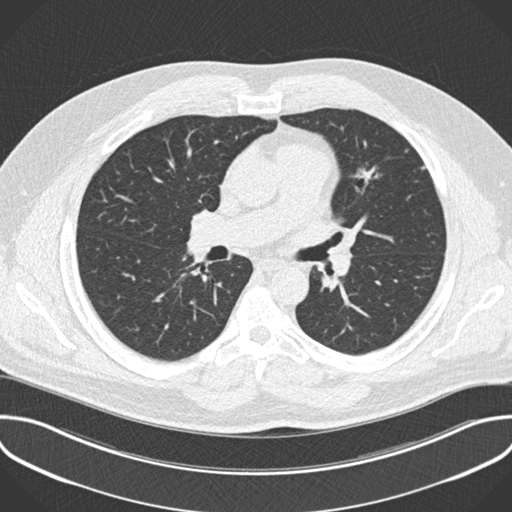
Low-dose screening chest CT, one axial slice; slice 124 of 201 in the series (ordered by position); reconstruction kernel B30f; 120 kVp; lung window (W 1500 / L -600 HU); 2 mm slice thickness; 512 × 512 image matrix, field of view 386 × 386 mm.
Structures marked on this image (expert manual segmentation):
- lesion 1 (tumor, upper lobe of left lung): bounding box <356,169,374,182> (left, top, right, bottom; pixels)